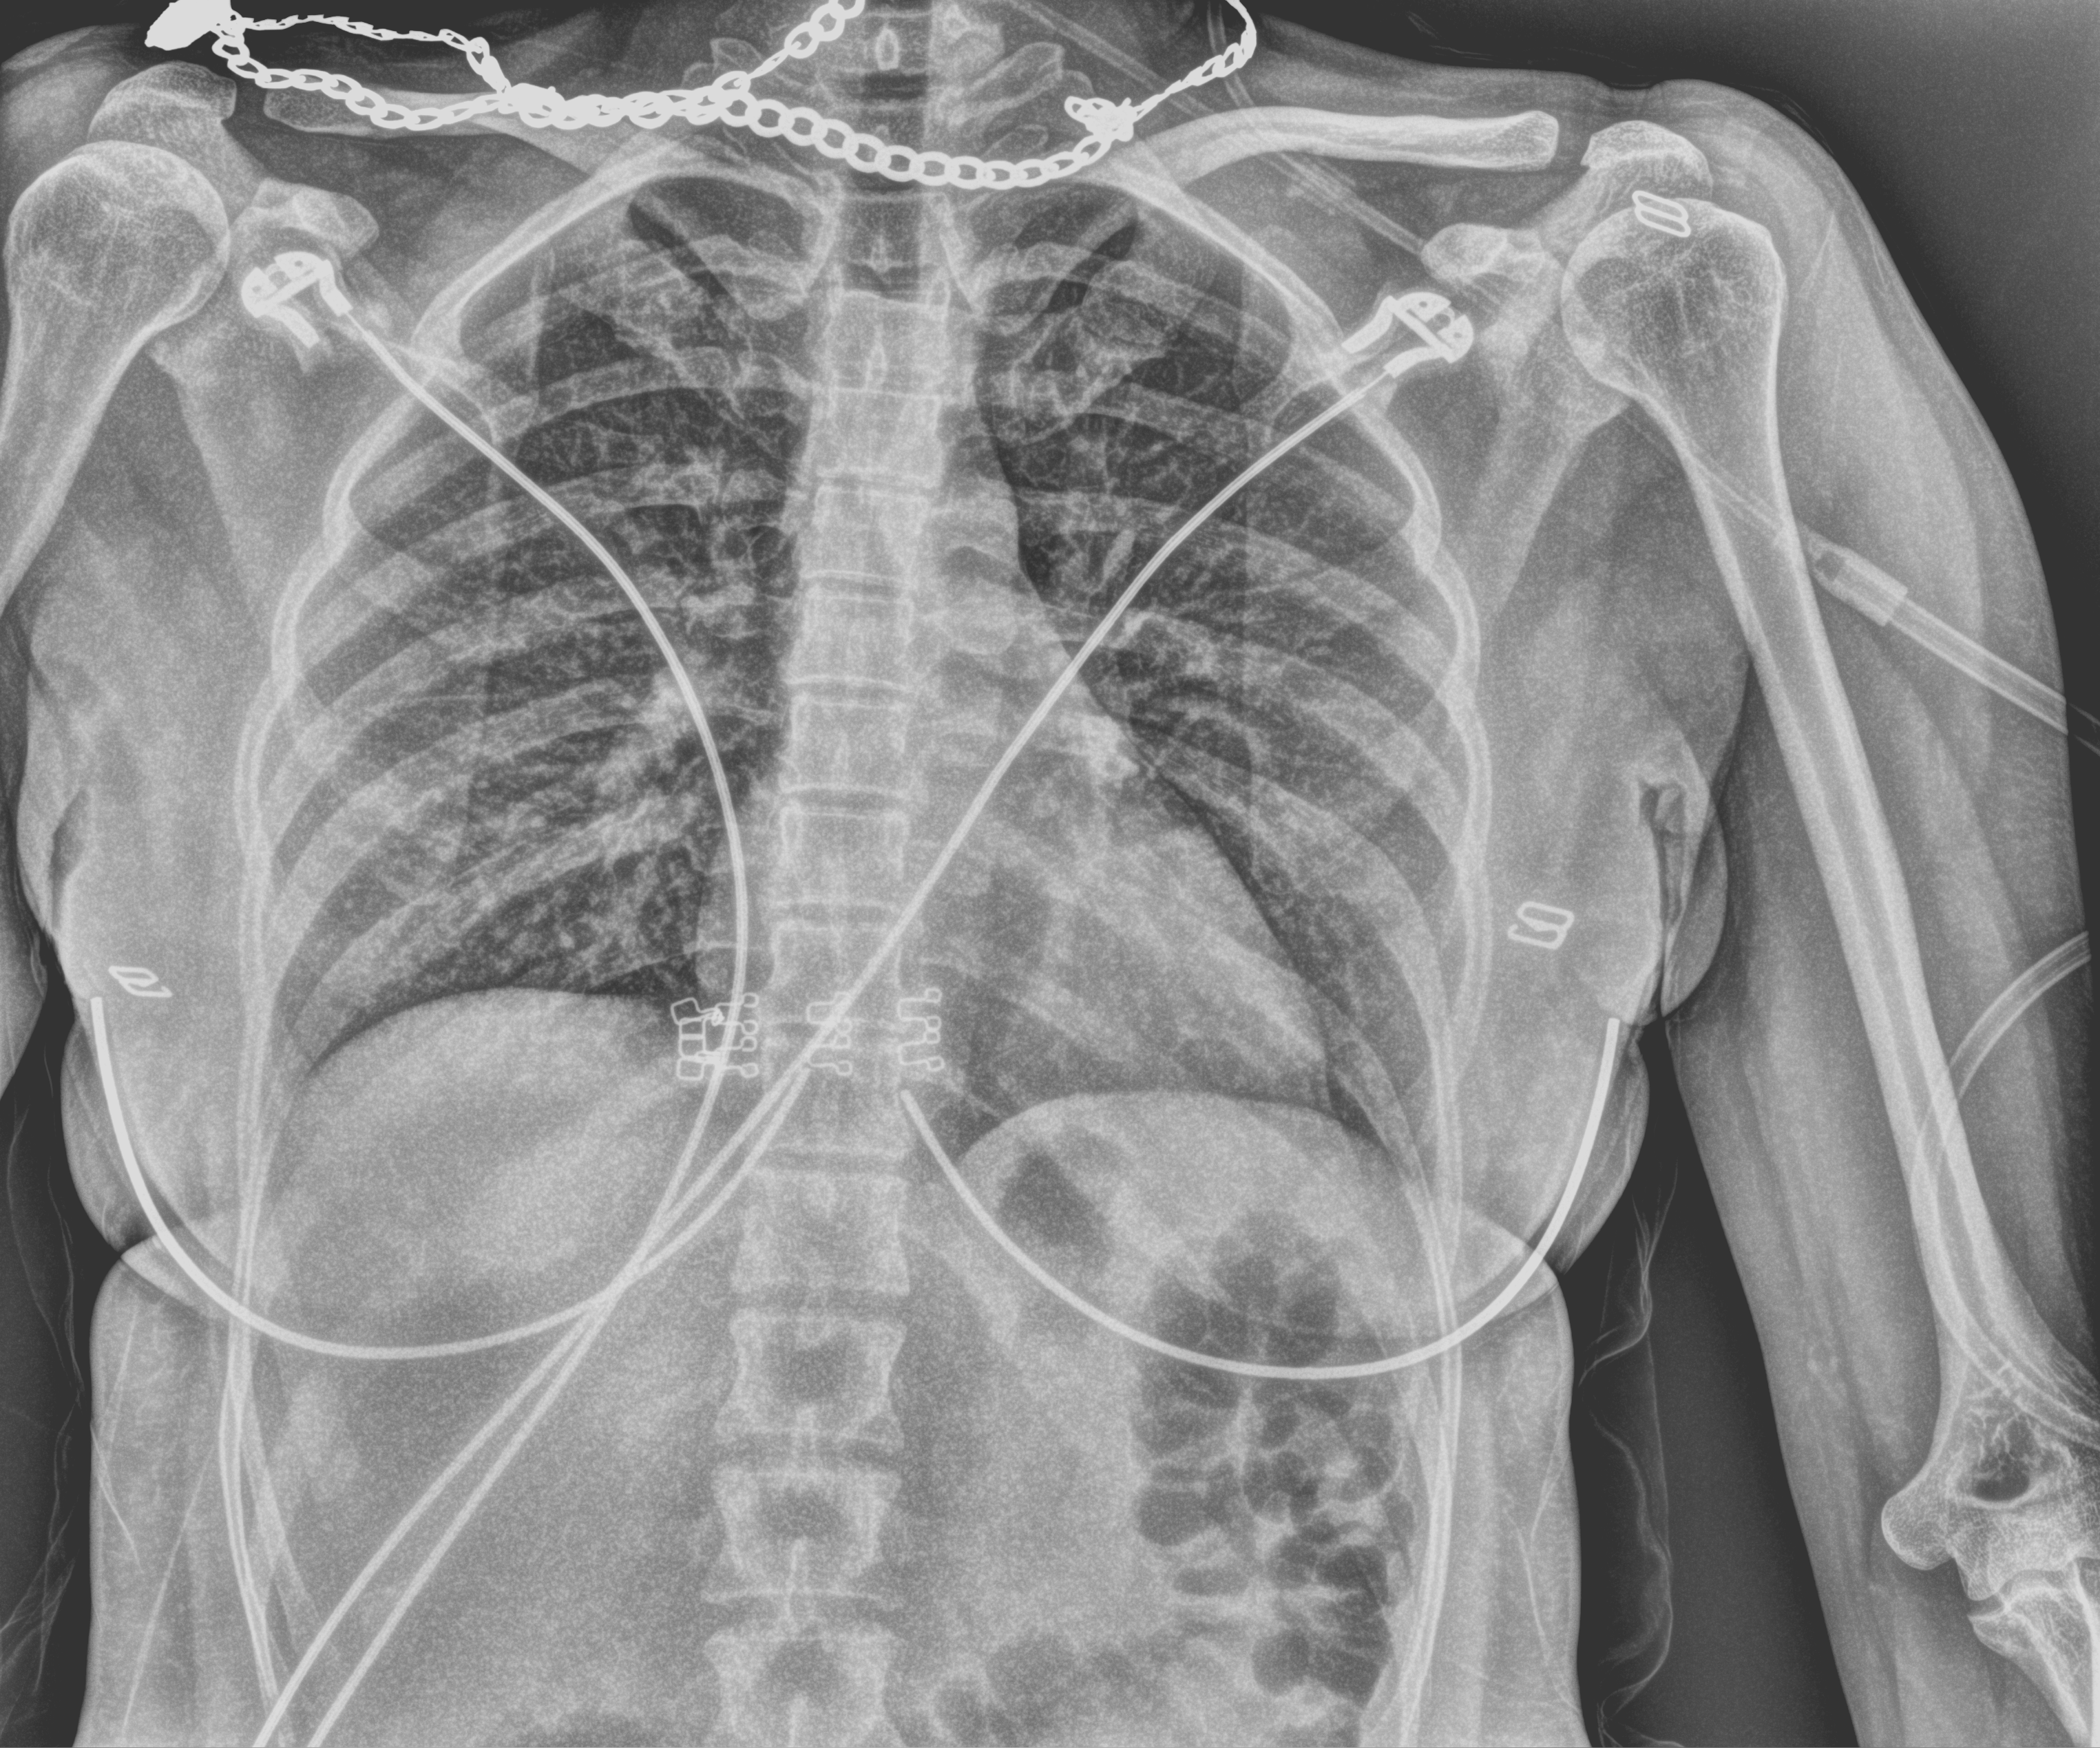
Portable chest radiograph, anteroposterior (AP) projection. Female patient hospitalised with COVID-19, age 18–59 years.
Hospital-stay facts (about this admission, not read from this image; timing relative to this image not recorded): admitted to intensive care during this hospital stay: no; mechanically ventilated during this hospital stay: no.